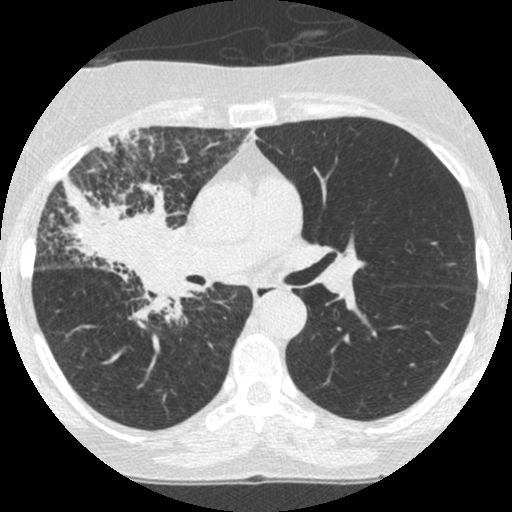
Low-dose screening chest CT, one axial slice. Slice 149 of 253 in the series (ordered by position). 120 kVp. Lung window (W 1500 / L -600 HU). 1.25 mm slice thickness. 512 × 512 image matrix, field of view 294 × 294 mm.
Outlined on this slice (outlined manually by an expert reader):
- lesion 2 (tumor, hilum of right lung): bounding box <49,168,188,340> (left, top, right, bottom; pixels)